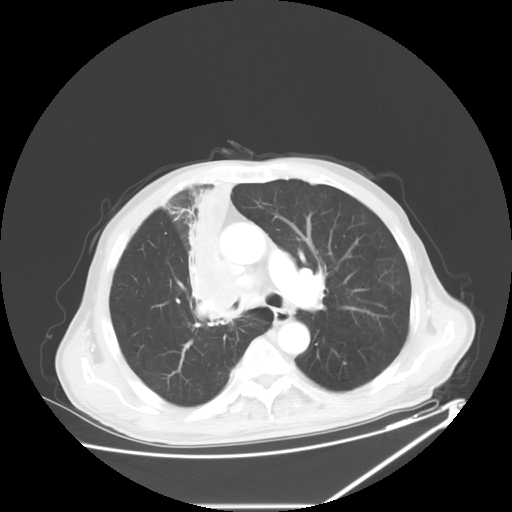
Chest CT, one axial slice. Reconstruction kernel STANDARD. Lung window (W 1500 / L -600 HU). 512 × 512 image matrix, field of view 410 × 410 mm. Patient: male, 73 years. Case-level facts recorded for this patient, not image findings: clinical TNM (as recorded): T2a N1 M0.
Outlined on this slice (rectangle marked by the reading radiologist):
- lung tumour (recorded histology: squamous cell carcinoma): bounding box (x1, y1, x2, y2) in pixels: (187, 166, 251, 326)